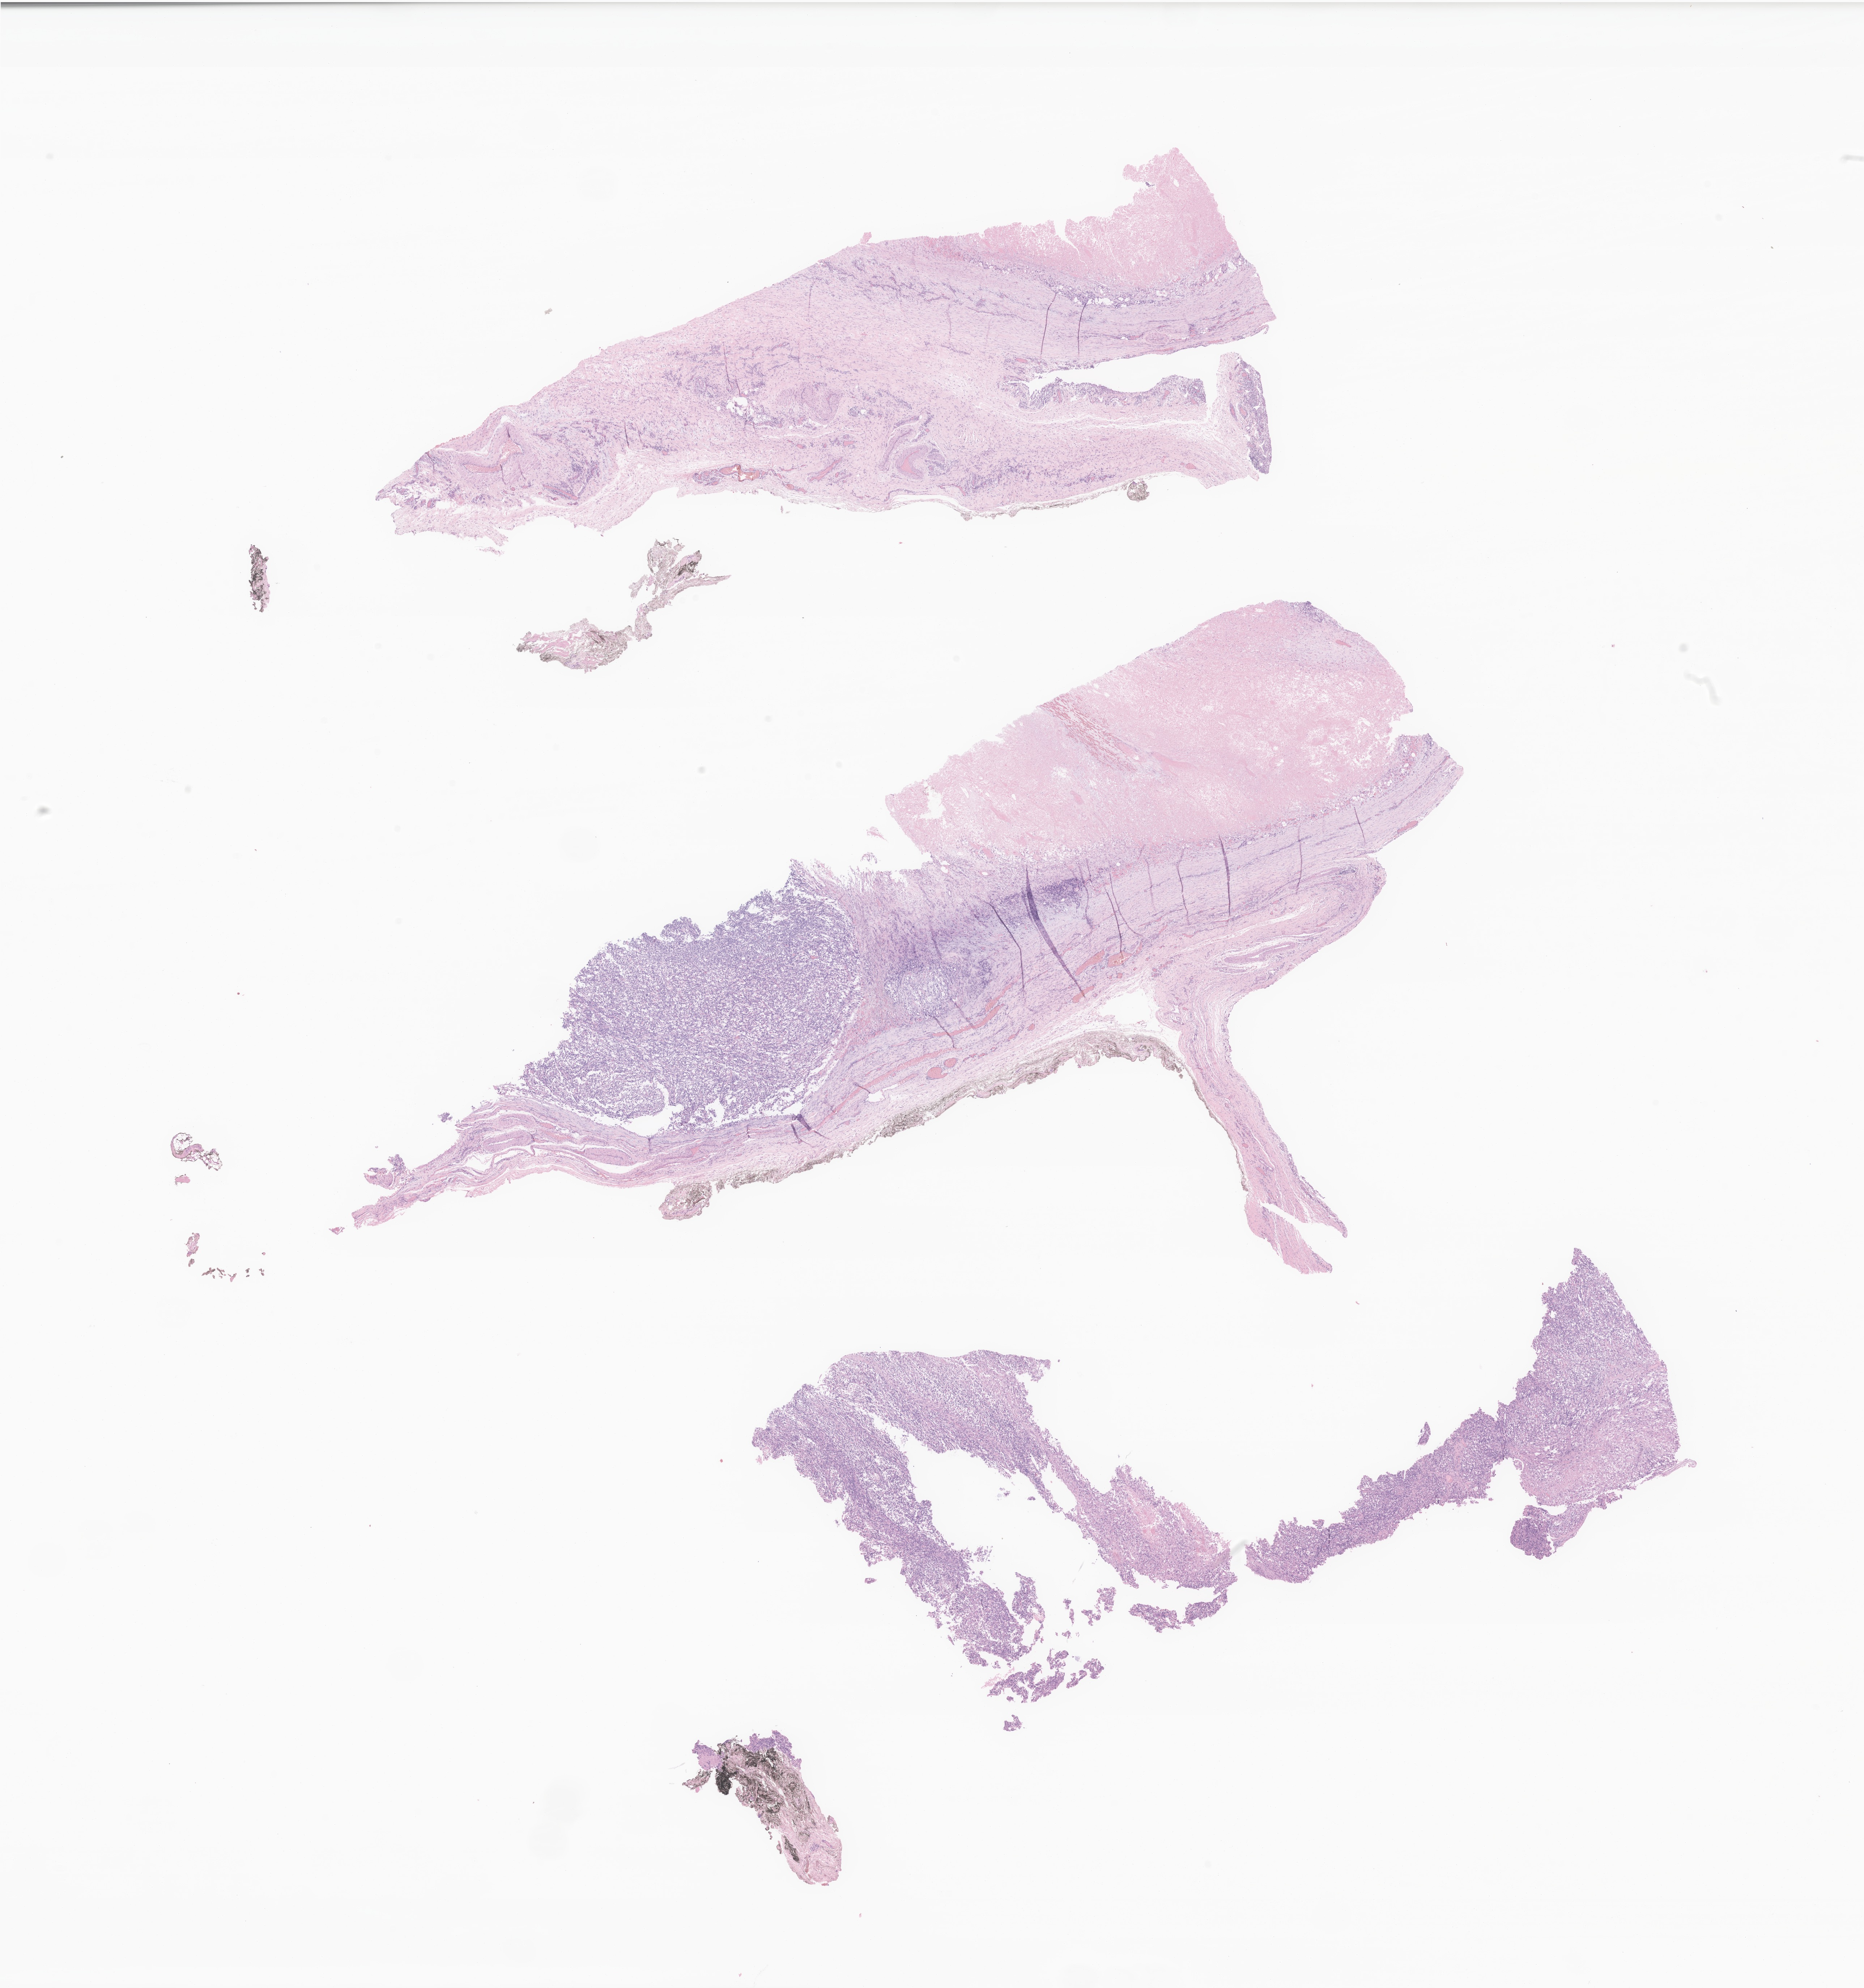
H&E whole-slide image of tumor tissue from the testis — a low-resolution overview of the entire scanned area, about 21.7 x 23.2 mm. FFPE section. Patient male; age 199 months (16 years 7 months).
• diagnosis: Rhabdomyosarcoma, NOS